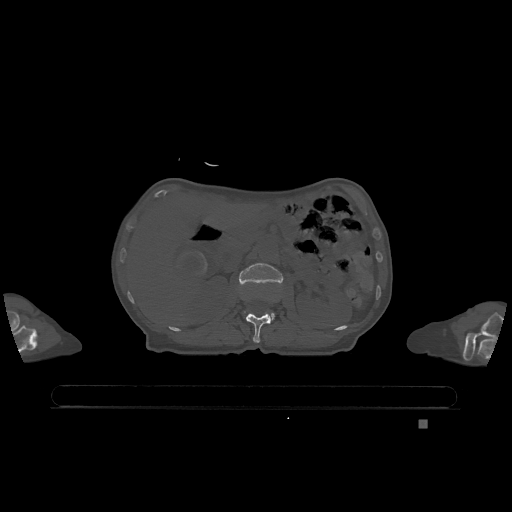
CT including the spine, one axial slice; position 453 of 1317 along the scan axis; bone window (W 1800 / L 400 HU); 0.5 mm slice thickness; 512 × 512 image matrix, field of view 500 × 500 mm. Patient: female, 74 years. Case-level facts recorded for this patient, not image findings: primary cancer: lung; vertebrae with lytic lesions (as recorded): T1, T4, T5, T6, L4, L5.
Structures marked on this image (semi-automatically segmented with operator editing):
- L1 vertebra: box from (x=246, y=313) to (x=271, y=343) px
- L2 vertebra: (x=239, y=263)–(x=283, y=321)